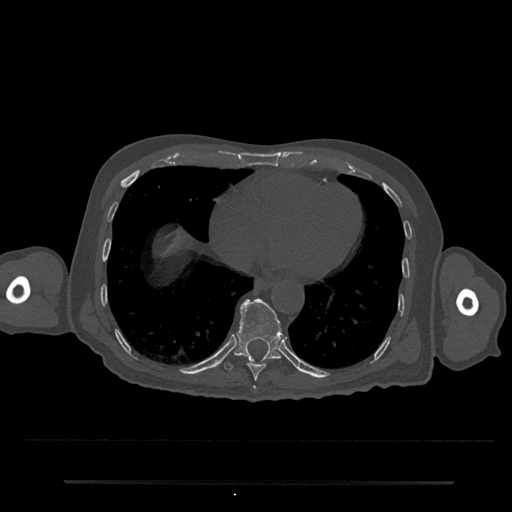
CT including the spine, one axial slice; slice 337 of 797 in the series (ordered by position); 120 kVp; bone window (W 1800 / L 400 HU); 512 × 512 image matrix. Male patient, age 74 years. From the clinical record (not read from this slice): primary cancer: prostate.
Structures marked on this image (semi-automatic segmentation, software-assisted and operator-edited):
- T10 vertebra: bounding box <224,298,283,371> (left, top, right, bottom; pixels)
- T8 vertebra: <253,386,256,389>
- T9 vertebra: <247,362,266,381>